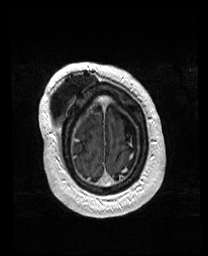
Brain MRI from a brain-tumour surgery series, one axial slice; slice 32 of 176 in the series (ordered by position); T1-weighted post-contrast; 208 × 256 image matrix. From the clinical record (not read from this slice): histopathology: Astrocytoma; WHO grade: 4; IDH mutation: yes; tumour location: Right Orbitofrontal Anterior Temporal Insular.
Annotated regions visible in this slice (outlined manually by an expert reader):
- previous resection cavity: box from (x=91, y=98) to (x=104, y=111) px